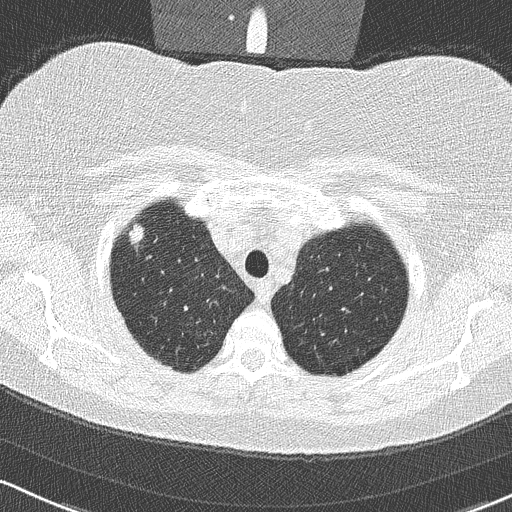
Low-dose screening chest CT, one axial slice. Position 272 of 315 along the scan axis. Reconstruction kernel B50f. Lung window (W 1500 / L -600 HU). 2 mm slice thickness. 512 × 512 image matrix, field of view 320 × 320 mm.
Annotated regions visible in this slice (expert manual segmentation):
- lesion 1 (tumor, upper lobe of right lung): bounding box <129,224,145,244> (left, top, right, bottom; pixels)